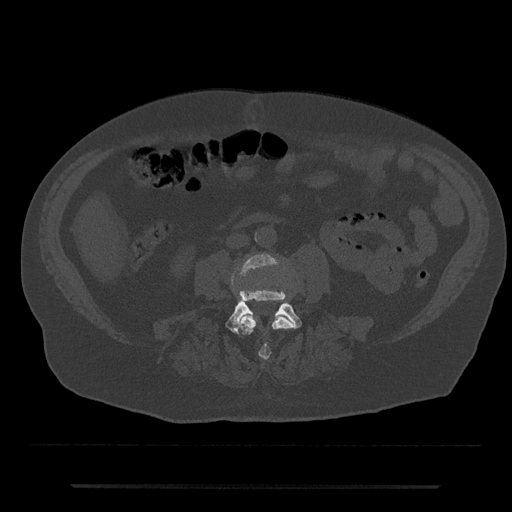
CT including the spine, one axial slice. Slice 375 of 797 in the series (ordered by position). Reconstruction kernel Br40s/3. 120 kVp. Bone window (W 1800 / L 400 HU). 512 × 512 image matrix, field of view 434 × 434 mm. Patient: male, 80 years. Case-level facts recorded for this patient, not image findings: primary cancer: prostate; vertebrae with lytic lesions (as recorded): L1, T11.
Outlined on this slice (semi-automatic segmentation, software-assisted and operator-edited):
- L3 vertebra: box from (x=231, y=254) to (x=294, y=360) px
- L4 vertebra: (x=225, y=290)–(x=302, y=334)